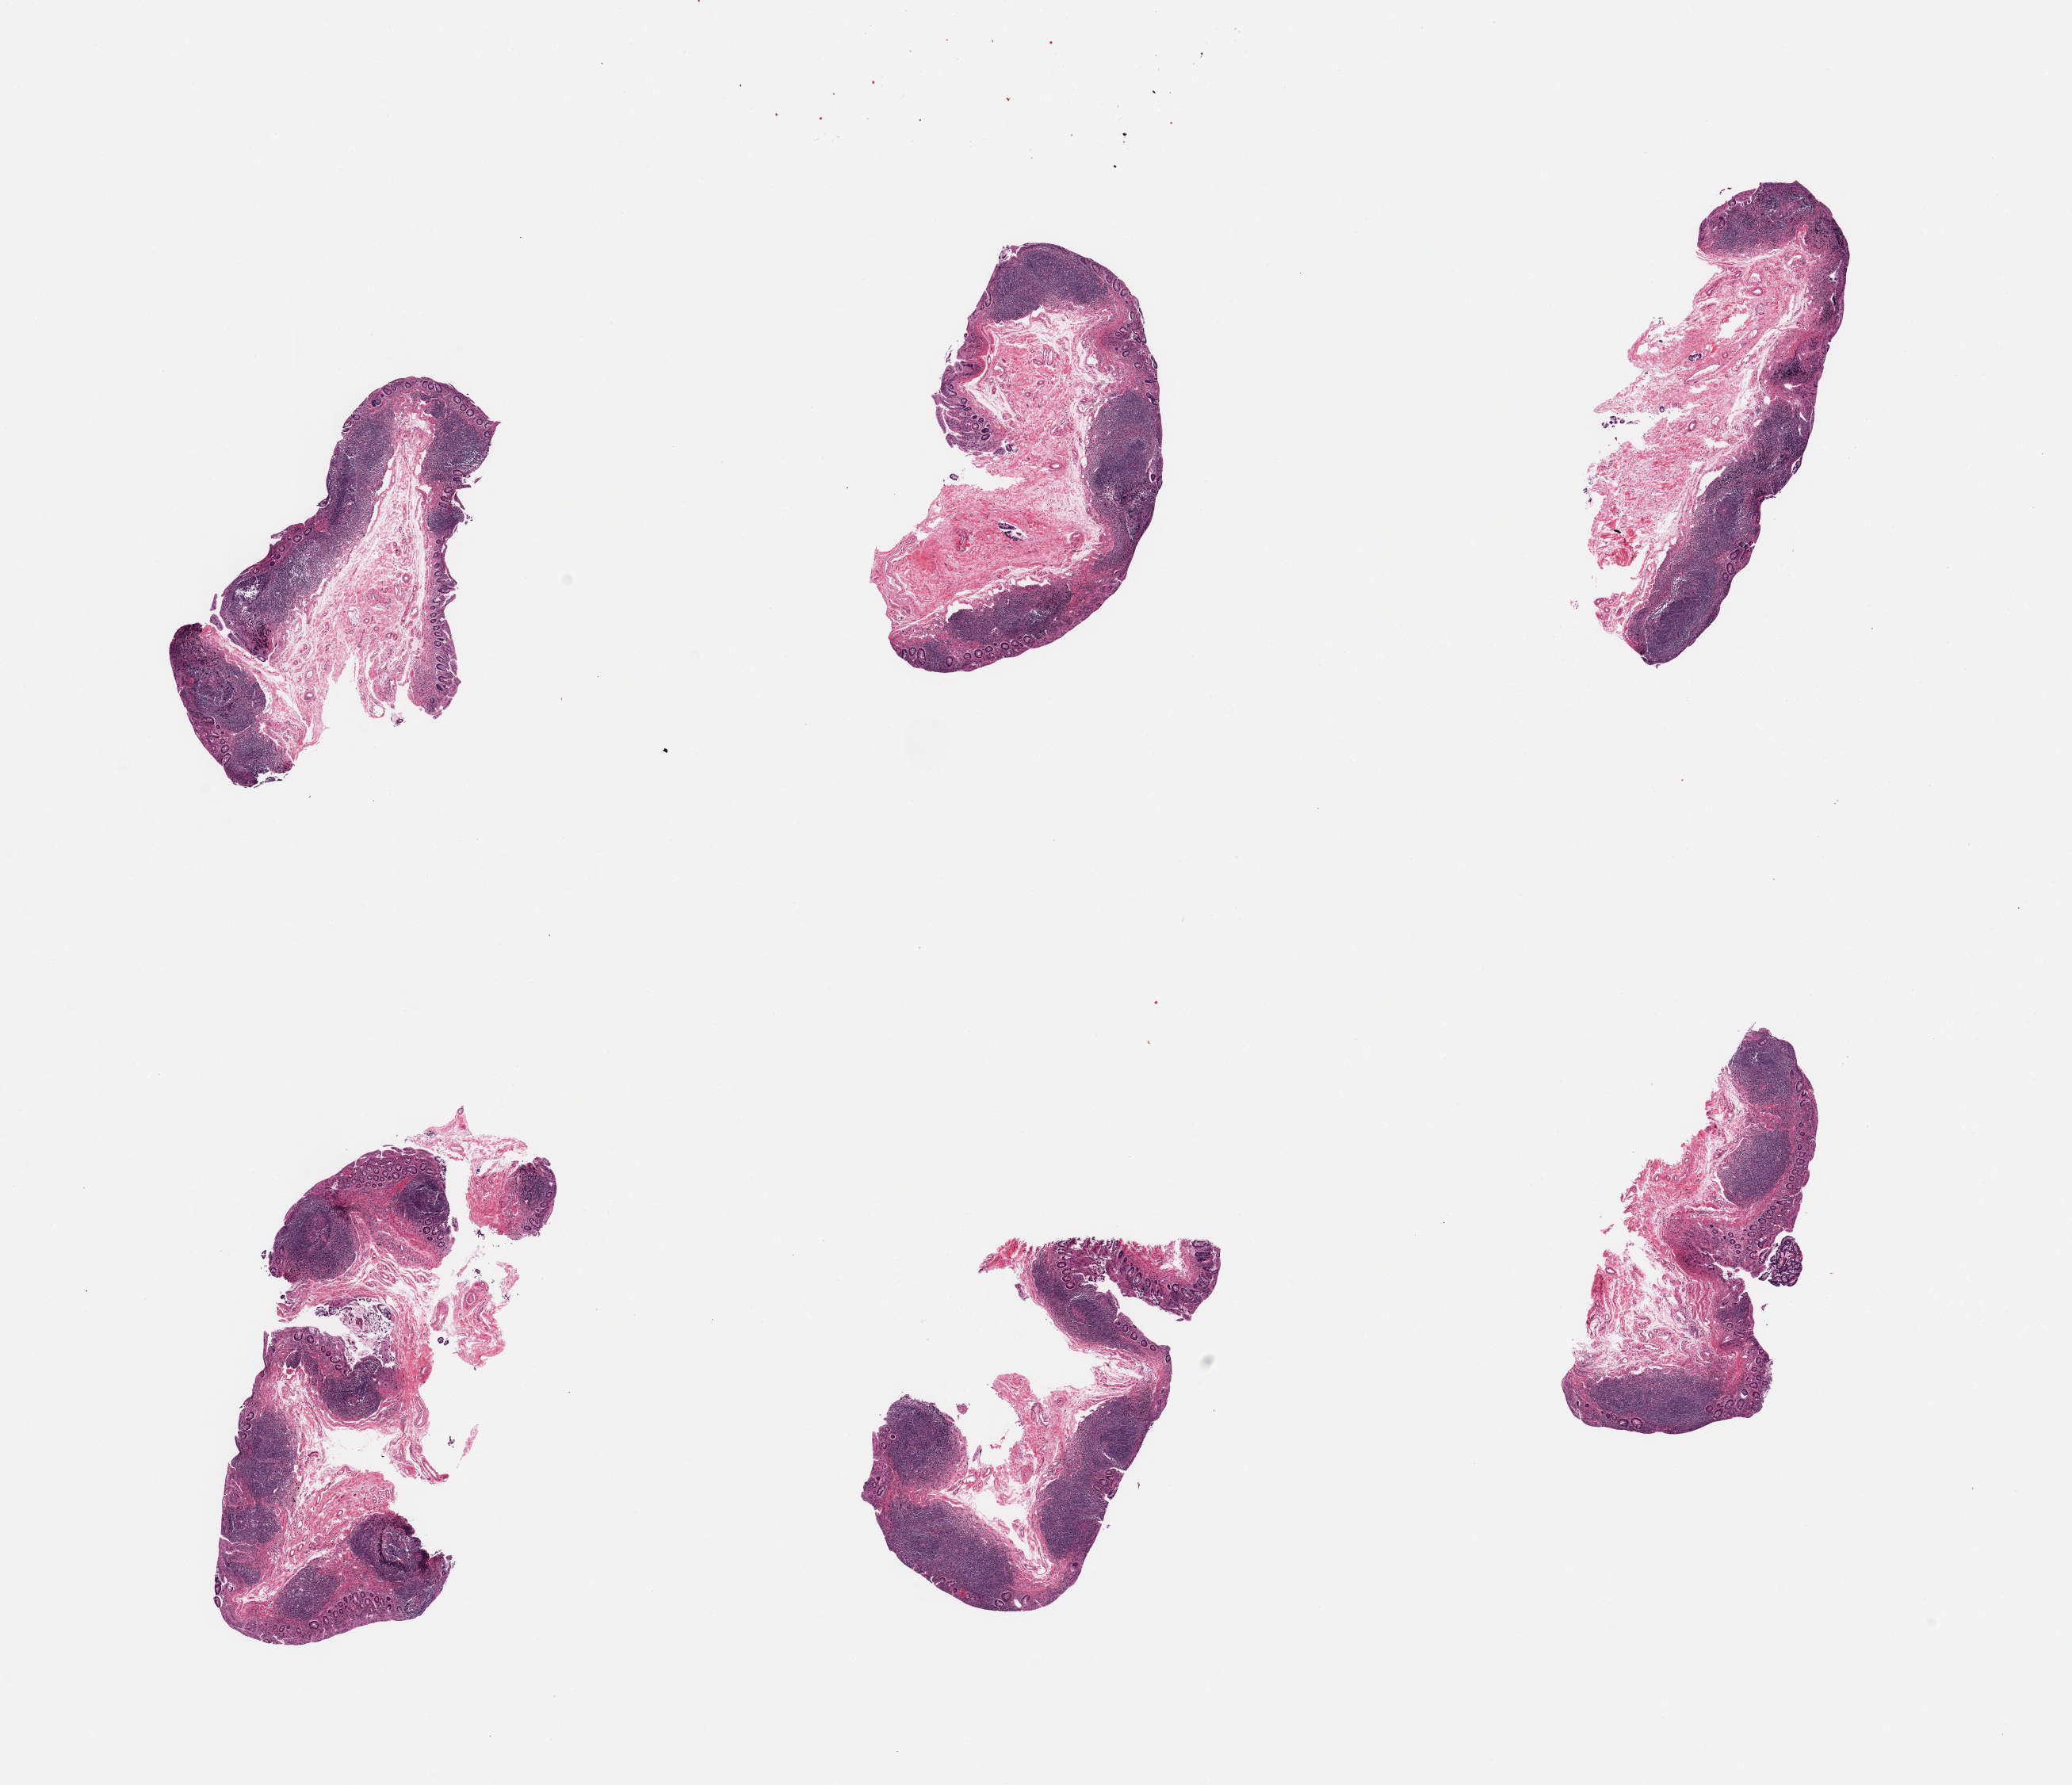
Whole-slide image, haematoxylin and eosin stain — whole scanned area (about 20.7 x 17.8 mm, slide scanned at 20x) shown as a low-resolution overview; PAXgene-fixed, paraffin-embedded tissue; sampled site (target tissue): ileum; tissue donor sample. Donor sex: female.
• pathologist's review note for this sample: 6 pieces, abundant lymphoid aggregates,, 40-50% of tissue rep dlineated